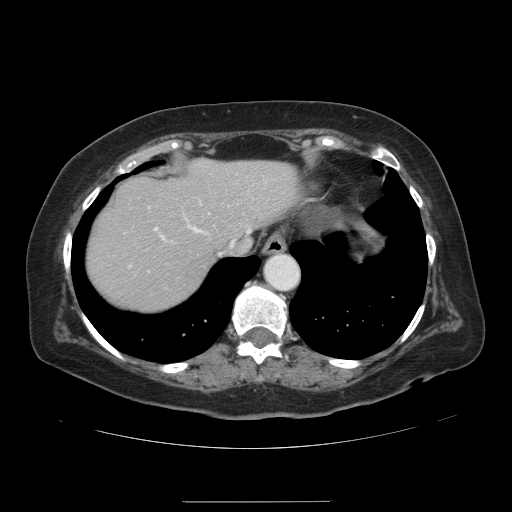
Contrast-enhanced abdominal CT, one axial slice; 120 kVp; intravenous contrast given; soft-tissue window (W 400 / L 40 HU); 512 × 512 image matrix, field of view 393 × 393 mm. Female patient, age 74 years. From the clinical record (not read from this slice): diagnosis: colorectal cancer liver metastases, imaged before liver resection; multiple liver metastases: yes.
Outlined on this slice (manually delineated by an expert):
- hepatic veins: box from (x=190, y=226) to (x=249, y=255) px
- liver: (x=87, y=160)–(x=298, y=311)
- planned liver remnant (the part of the liver to remain after resection): (x=87, y=160)–(x=298, y=311)
- portal vein (with intrahepatic branches): (x=154, y=227)–(x=164, y=238)